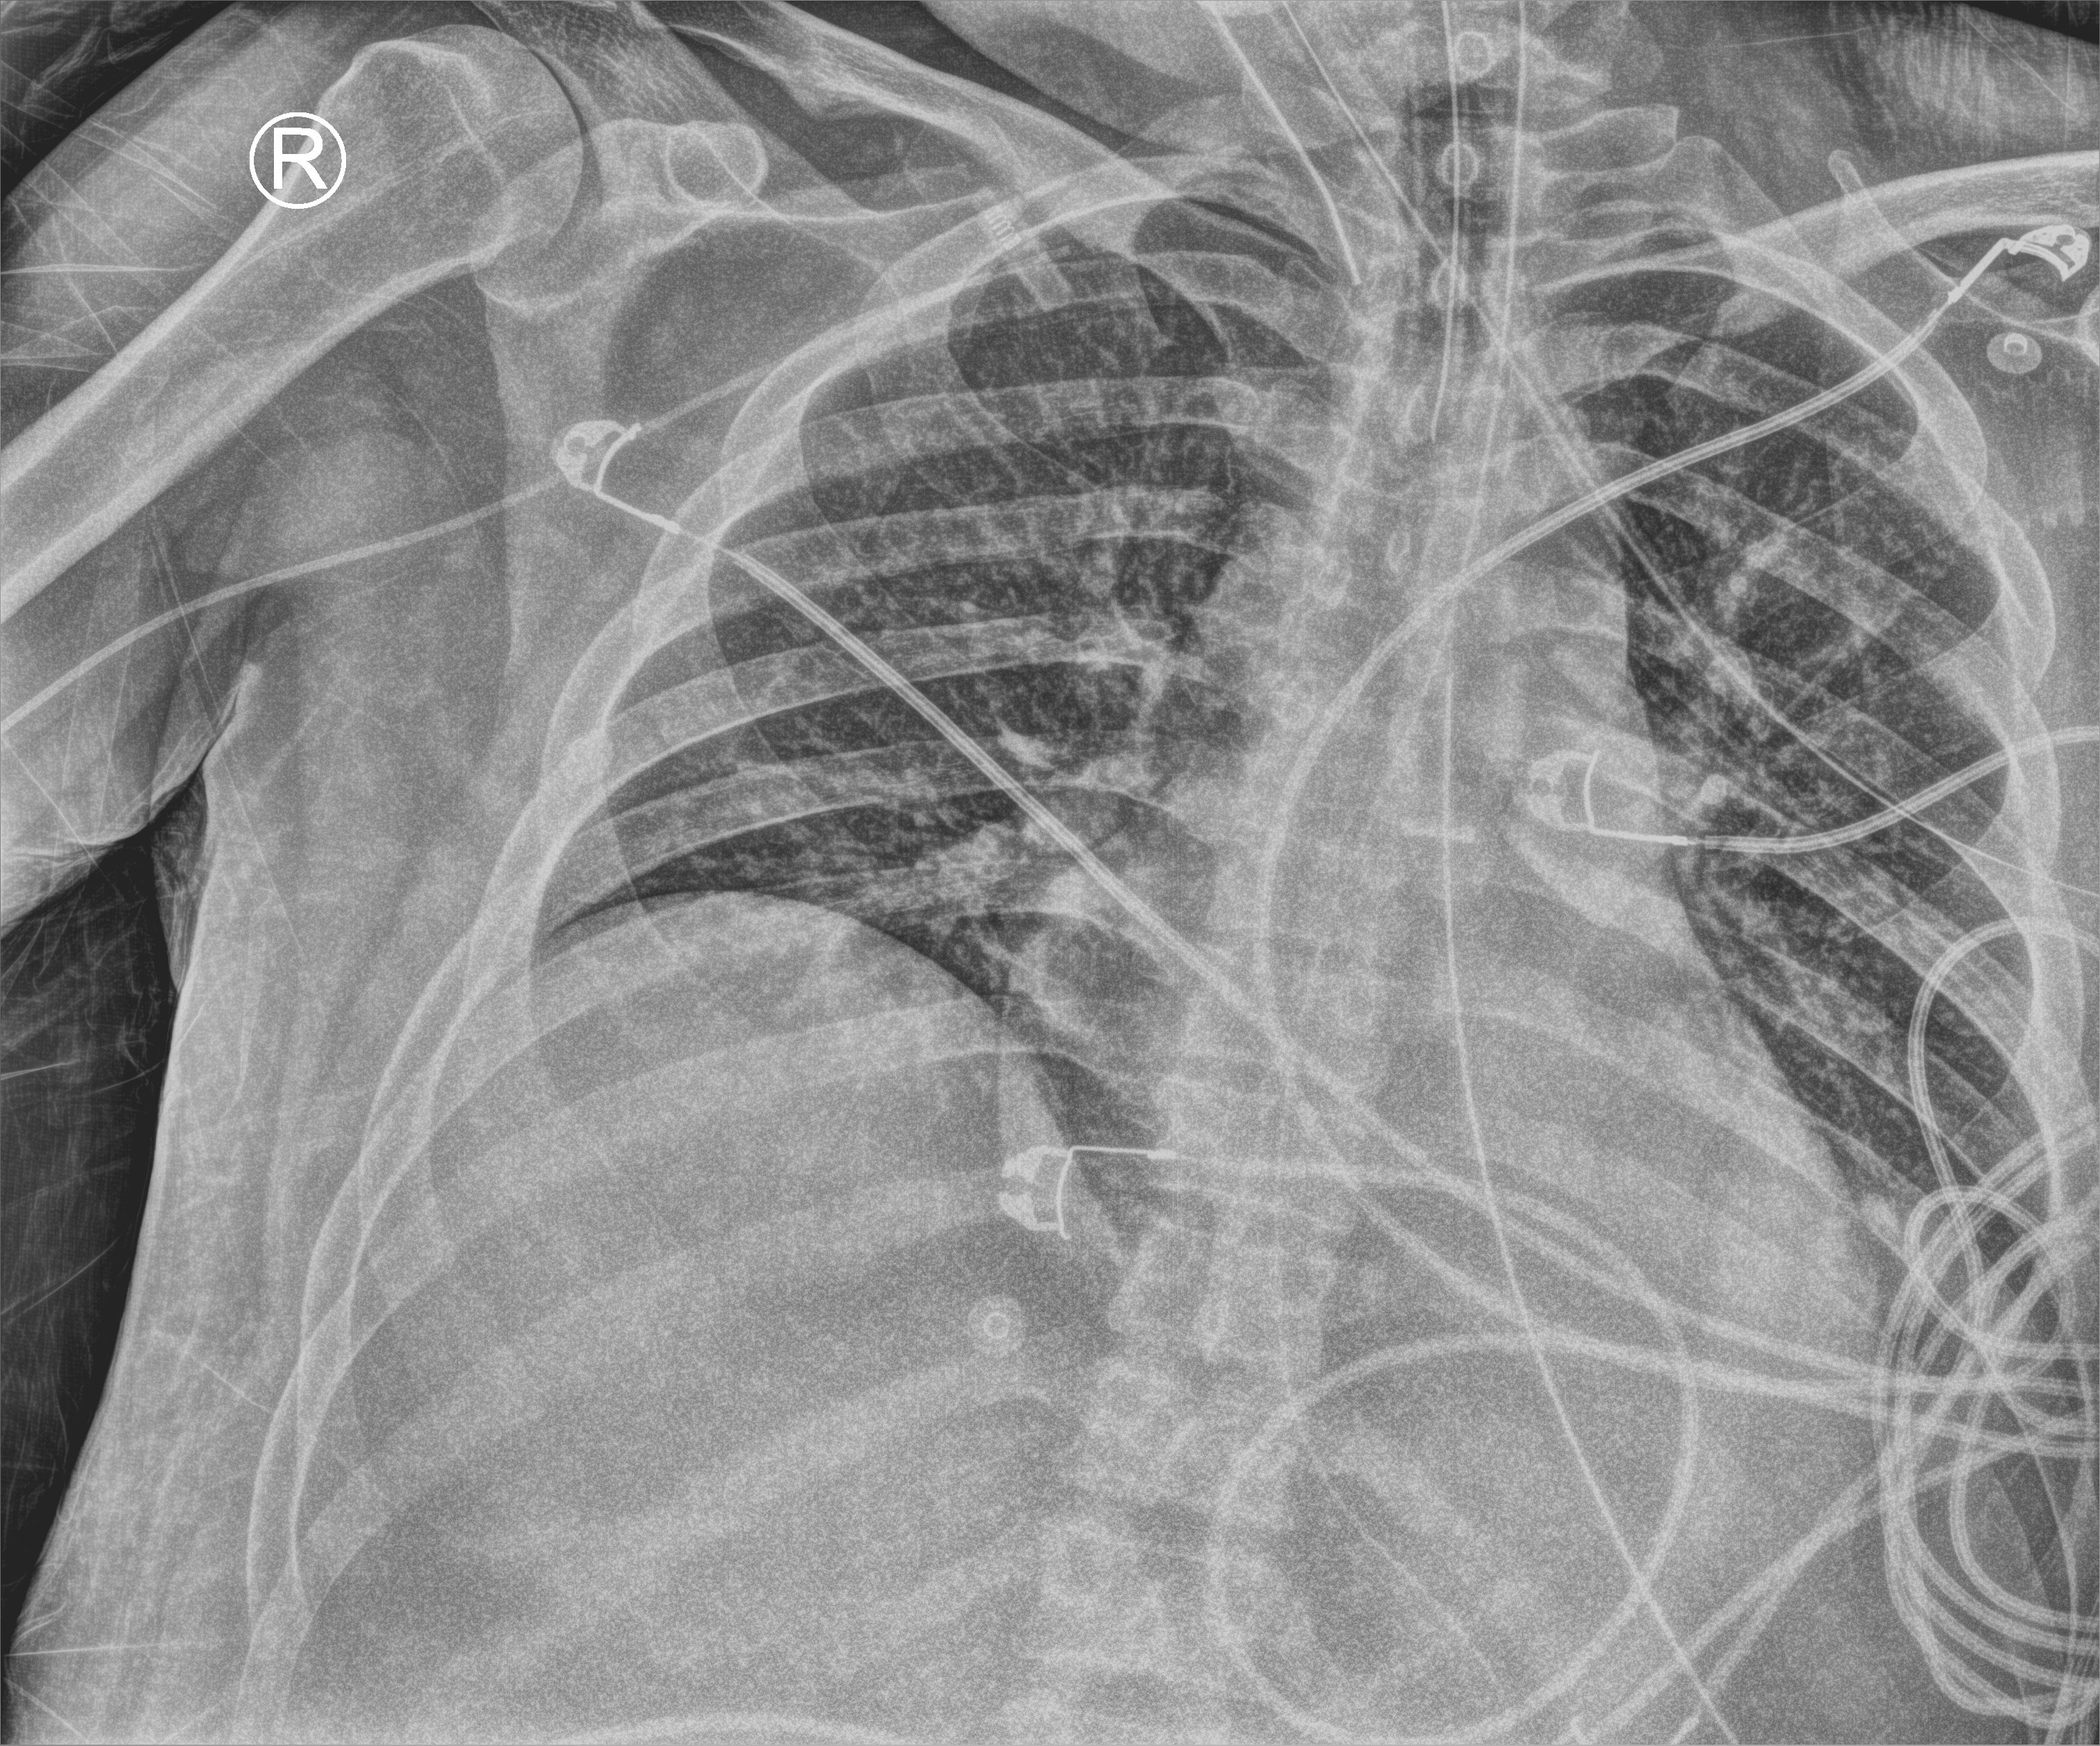
Portable chest radiograph; anteroposterior (AP) projection. Patient hospitalised with COVID-19; male, aged 18–59 years.
From the hospital-stay record, not from the radiograph (when in the stay this image was taken is not recorded): other chronic lung disease (admission record): no.